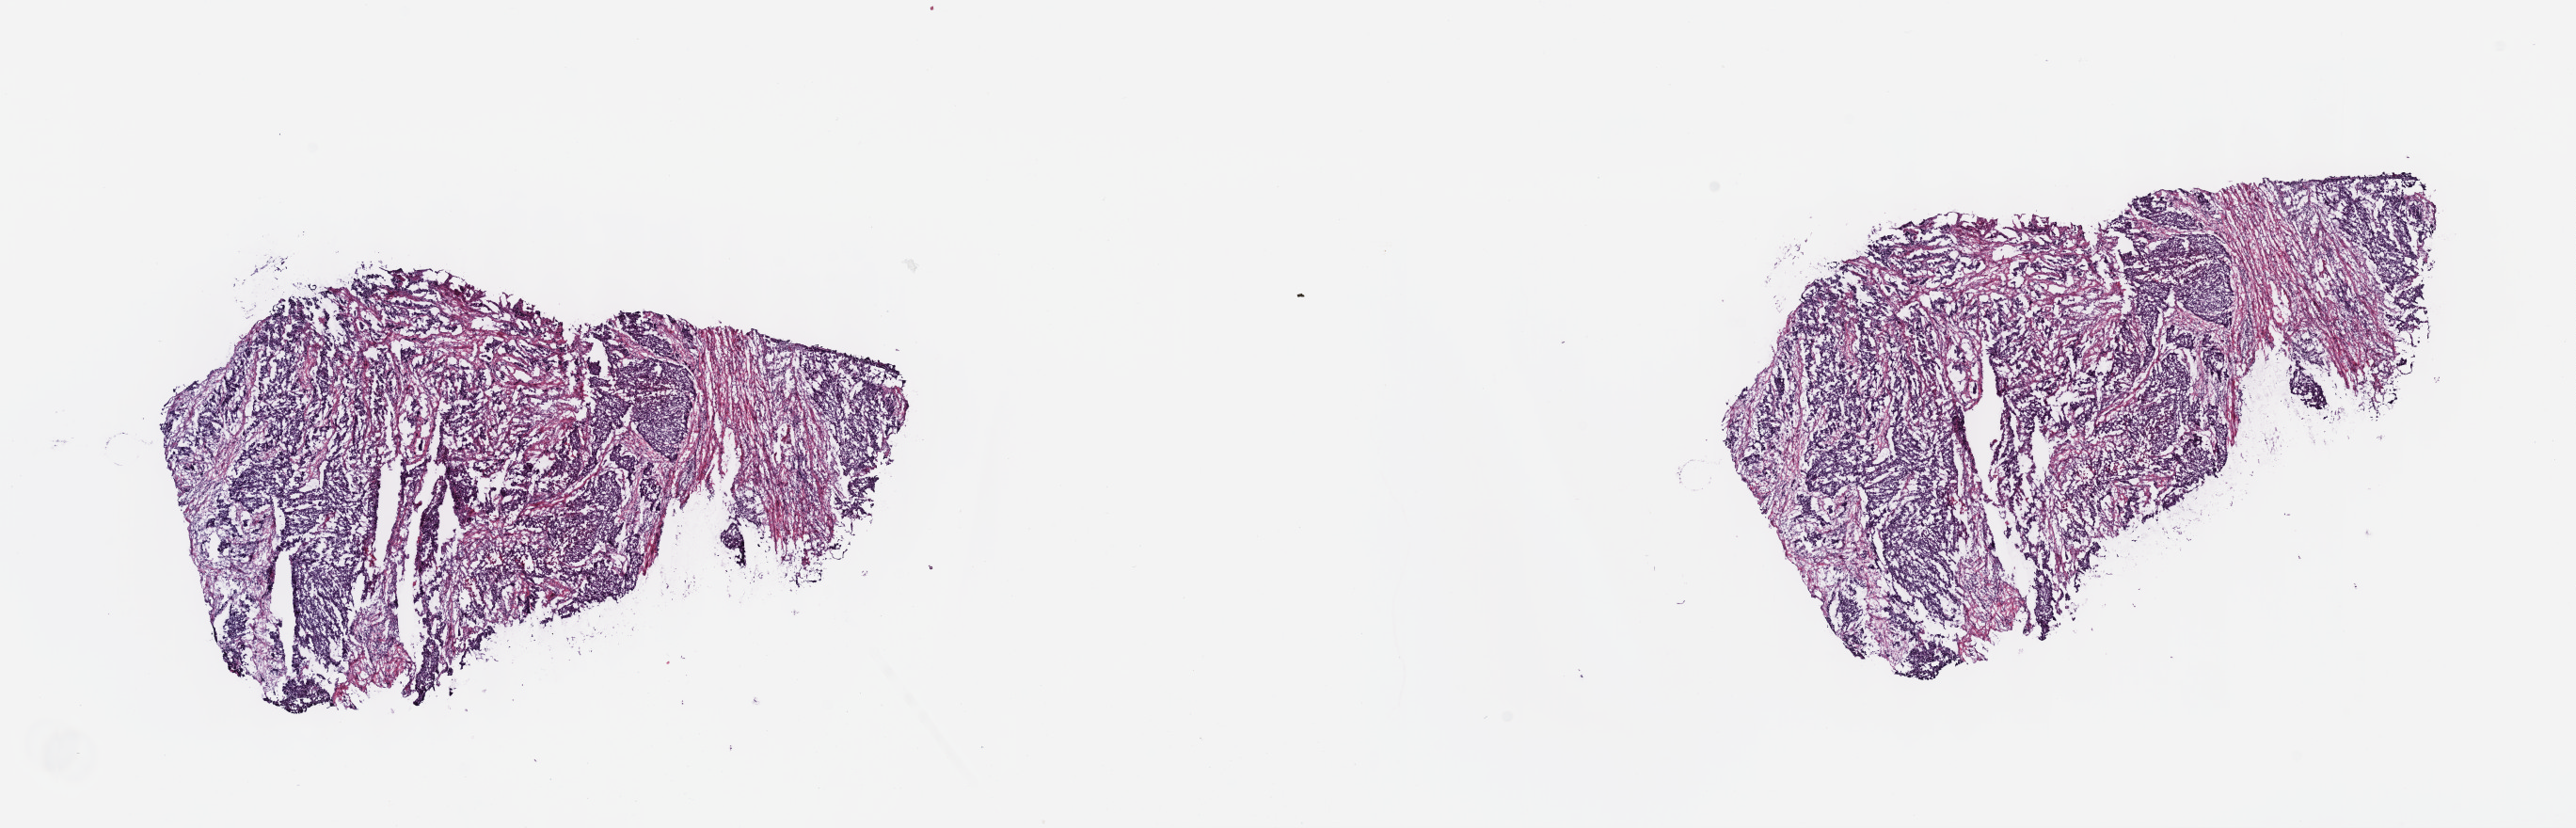
Digitized Hematoxylin and eosin (H&E) stained tissue section (whole slide) — low-resolution overview of the scanned area, about 22.1 x 7.1 mm (from a 40x scan); frozen section; primary tumour sample from the esophagus. Patient: male, age at initial diagnosis 47 years. Pathologist review of this section (percent, as recorded): tumour cells 100%, tumour nuclei 65%.
Histologic diagnosis: Squamous cell carcinoma, NOS (lower third of esophagus).